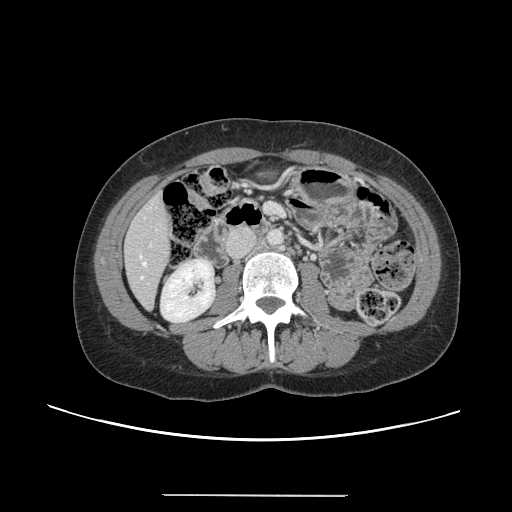
Contrast-enhanced abdominal CT, one axial slice; slice 39 of 144 in the series (ordered by position); 120 kVp; soft-tissue window (W 400 / L 40 HU); 2.5 mm slice thickness; 512 × 512 image matrix, field of view 380 × 380 mm. Female patient, age 53 years. From the clinical record (not read from this slice): diagnosis: colorectal cancer liver metastases, imaged before liver resection; multiple liver metastases: yes; largest metastasis: 1.1 cm; disease in both lobes: no.
Annotated regions visible in this slice (manually delineated by an expert):
- hepatic veins: box from (x=140, y=255) to (x=146, y=279) px
- liver: (x=125, y=194)–(x=170, y=308)
- planned liver remnant (the part of the liver to remain after resection): (x=125, y=193)–(x=170, y=308)
- portal vein (with intrahepatic branches): (x=149, y=244)–(x=152, y=247)